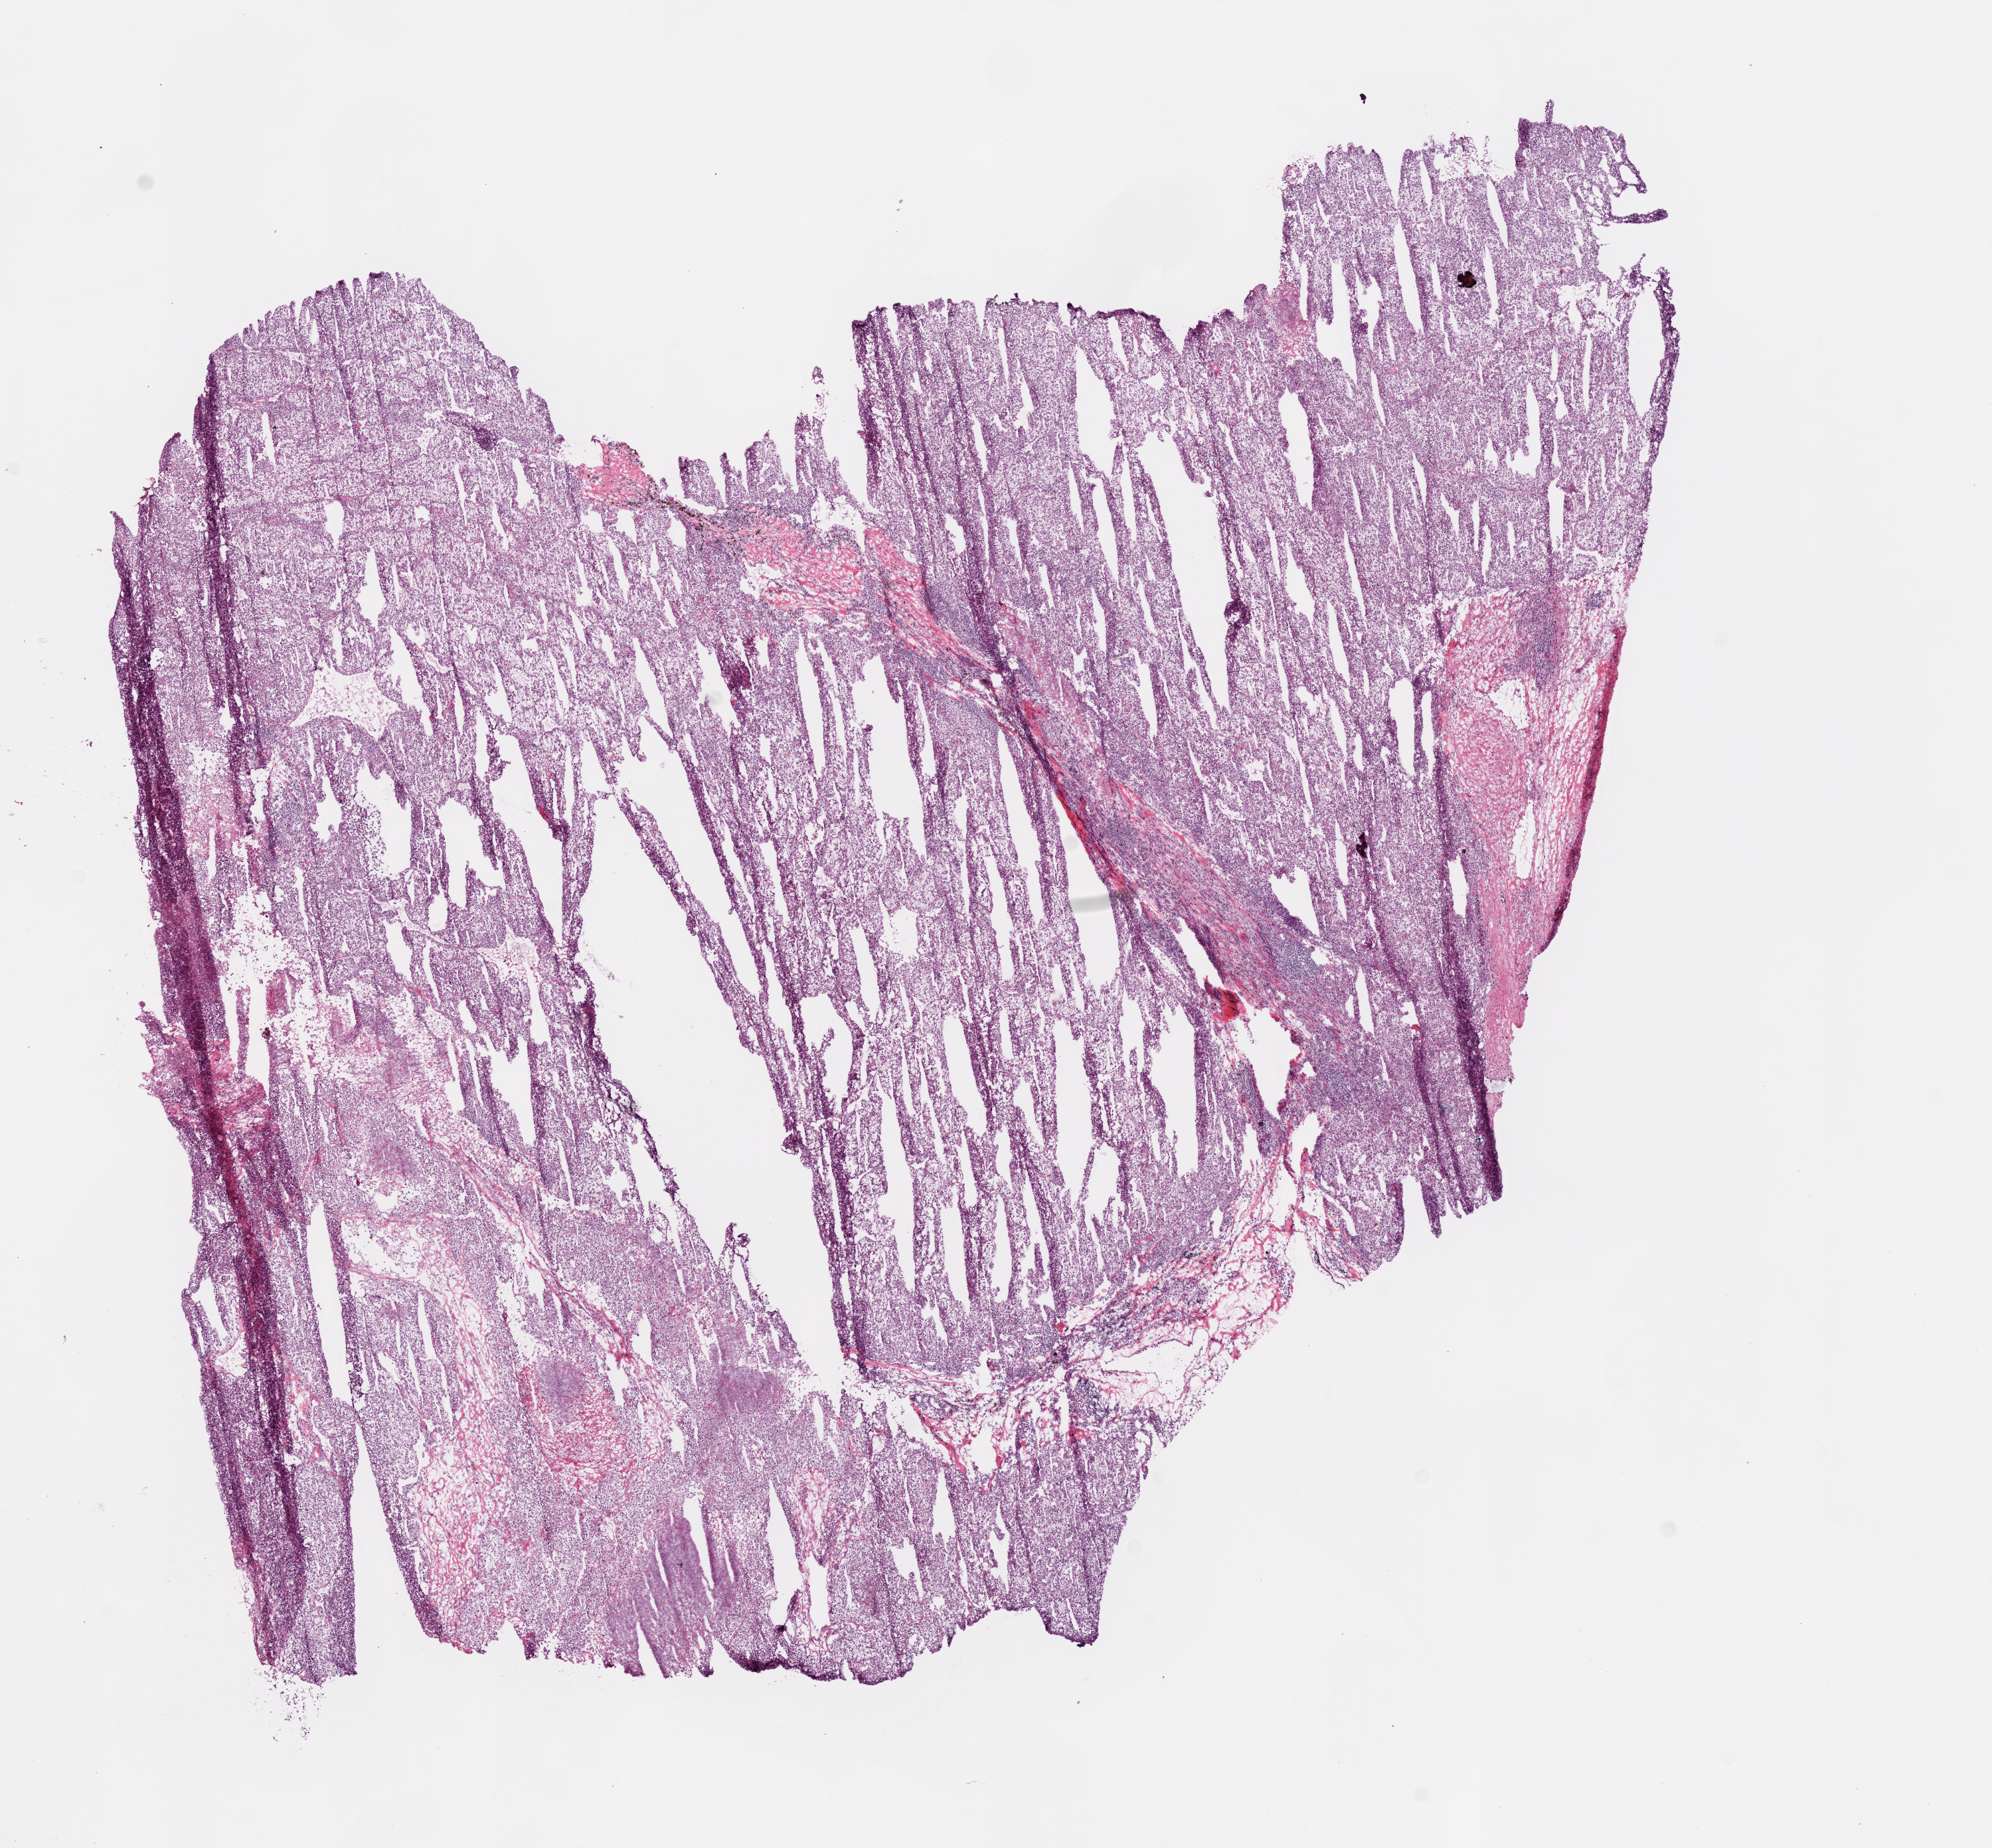
Digitized Hematoxylin and eosin (H&E) stained tissue section (whole slide), low-resolution overview of the scanned area, about 12.0 x 11.2 mm (from a 20x scan). Frozen section. Primary tumour sample from the kidney. Male patient; age at initial diagnosis 60 years. Histologic grade: G3 (poorly differentiated). Slide review estimates, as recorded: tumour cells 90%, tumour nuclei 80%, normal cells 0%, stromal cells 10%, necrosis 0%.
- TNM: T1 N0 M0
- AJCC pathologic stage: I
- laterality: left
- pathologic diagnosis: Clear cell adenocarcinoma, NOS